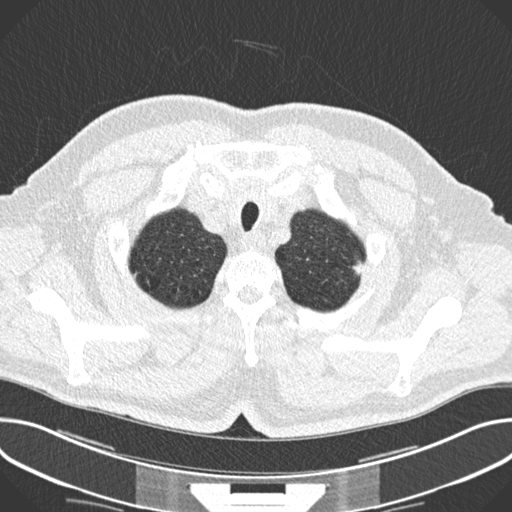
Low-dose screening chest CT, one axial slice. 120 kVp. Lung window (W 1500 / L -600 HU). 2 mm slice thickness. 512 × 512 image matrix, field of view 380 × 380 mm.
Outlined on this slice (manually delineated by an expert):
- lesion 1 (tumor, upper lobe of left lung): bounding box [x1, y1, x2, y2] px = [352, 261, 364, 276]